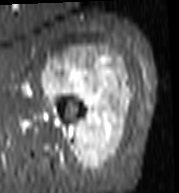
MRI of an extremity soft-tissue mass, one axial slice. Slice 76 of 103 in the series (ordered by position). STIR. MR volume resampled by the dataset authors to the PET/CT grid (not the native acquisition matrix). 3.27 mm slice thickness. 179 × 193 image matrix, field of view 175 × 188 mm. Female patient. From the clinical record (not read from this slice): histological type: undifferentiated – high grade; grade: high; site of the primary tumour: left thigh.
Annotated regions visible in this slice (expert contour drawn on MRI and transferred to this co-registered scan by the dataset authors):
- gross tumour volume including surrounding oedema: box from (x=41, y=46) to (x=131, y=170) px
- gross tumour volume (mass): (x=41, y=46)–(x=131, y=170)